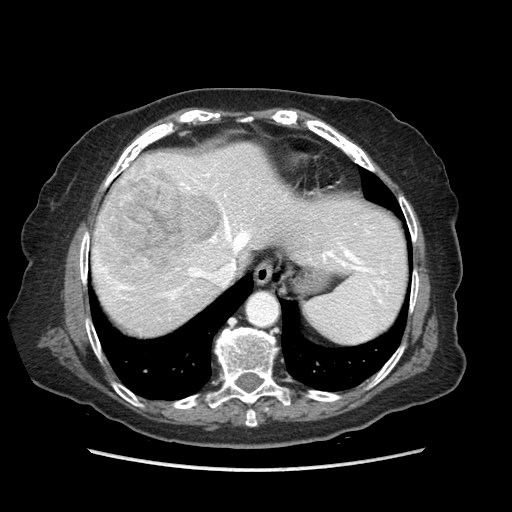
Contrast-enhanced abdominal CT (liver protocol), one axial slice. Slice 68 of 89 in the series (ordered by position). Reconstruction kernel STANDARD. 140 kVp. Soft-tissue window (W 400 / L 40 HU). 2.5 mm slice thickness. 512 × 512 image matrix, field of view 360 × 360 mm. Case-level facts recorded for this patient, not image findings: diagnosis: hepatocellular carcinoma (patient treated with transarterial chemoembolisation; whether this scan precedes or follows treatment is not stated here); TNM stage (as recorded): Stage-IIIA; Child-Pugh class: A; tumour differentiation: well differentiated; tumour nodularity: multinodular.
Structures marked on this image (semi-automatic segmentation, software-assisted and operator-edited):
- abdominal aorta: bounding box <248,294,277,325> (left, top, right, bottom; pixels)
- liver parenchyma outside the tumour (the mass and vessels are separate outlines, so this box may not span the whole liver): <92,142,404,336>
- mass: <96,168,218,284>
- liver vessels: <96,173,370,300>